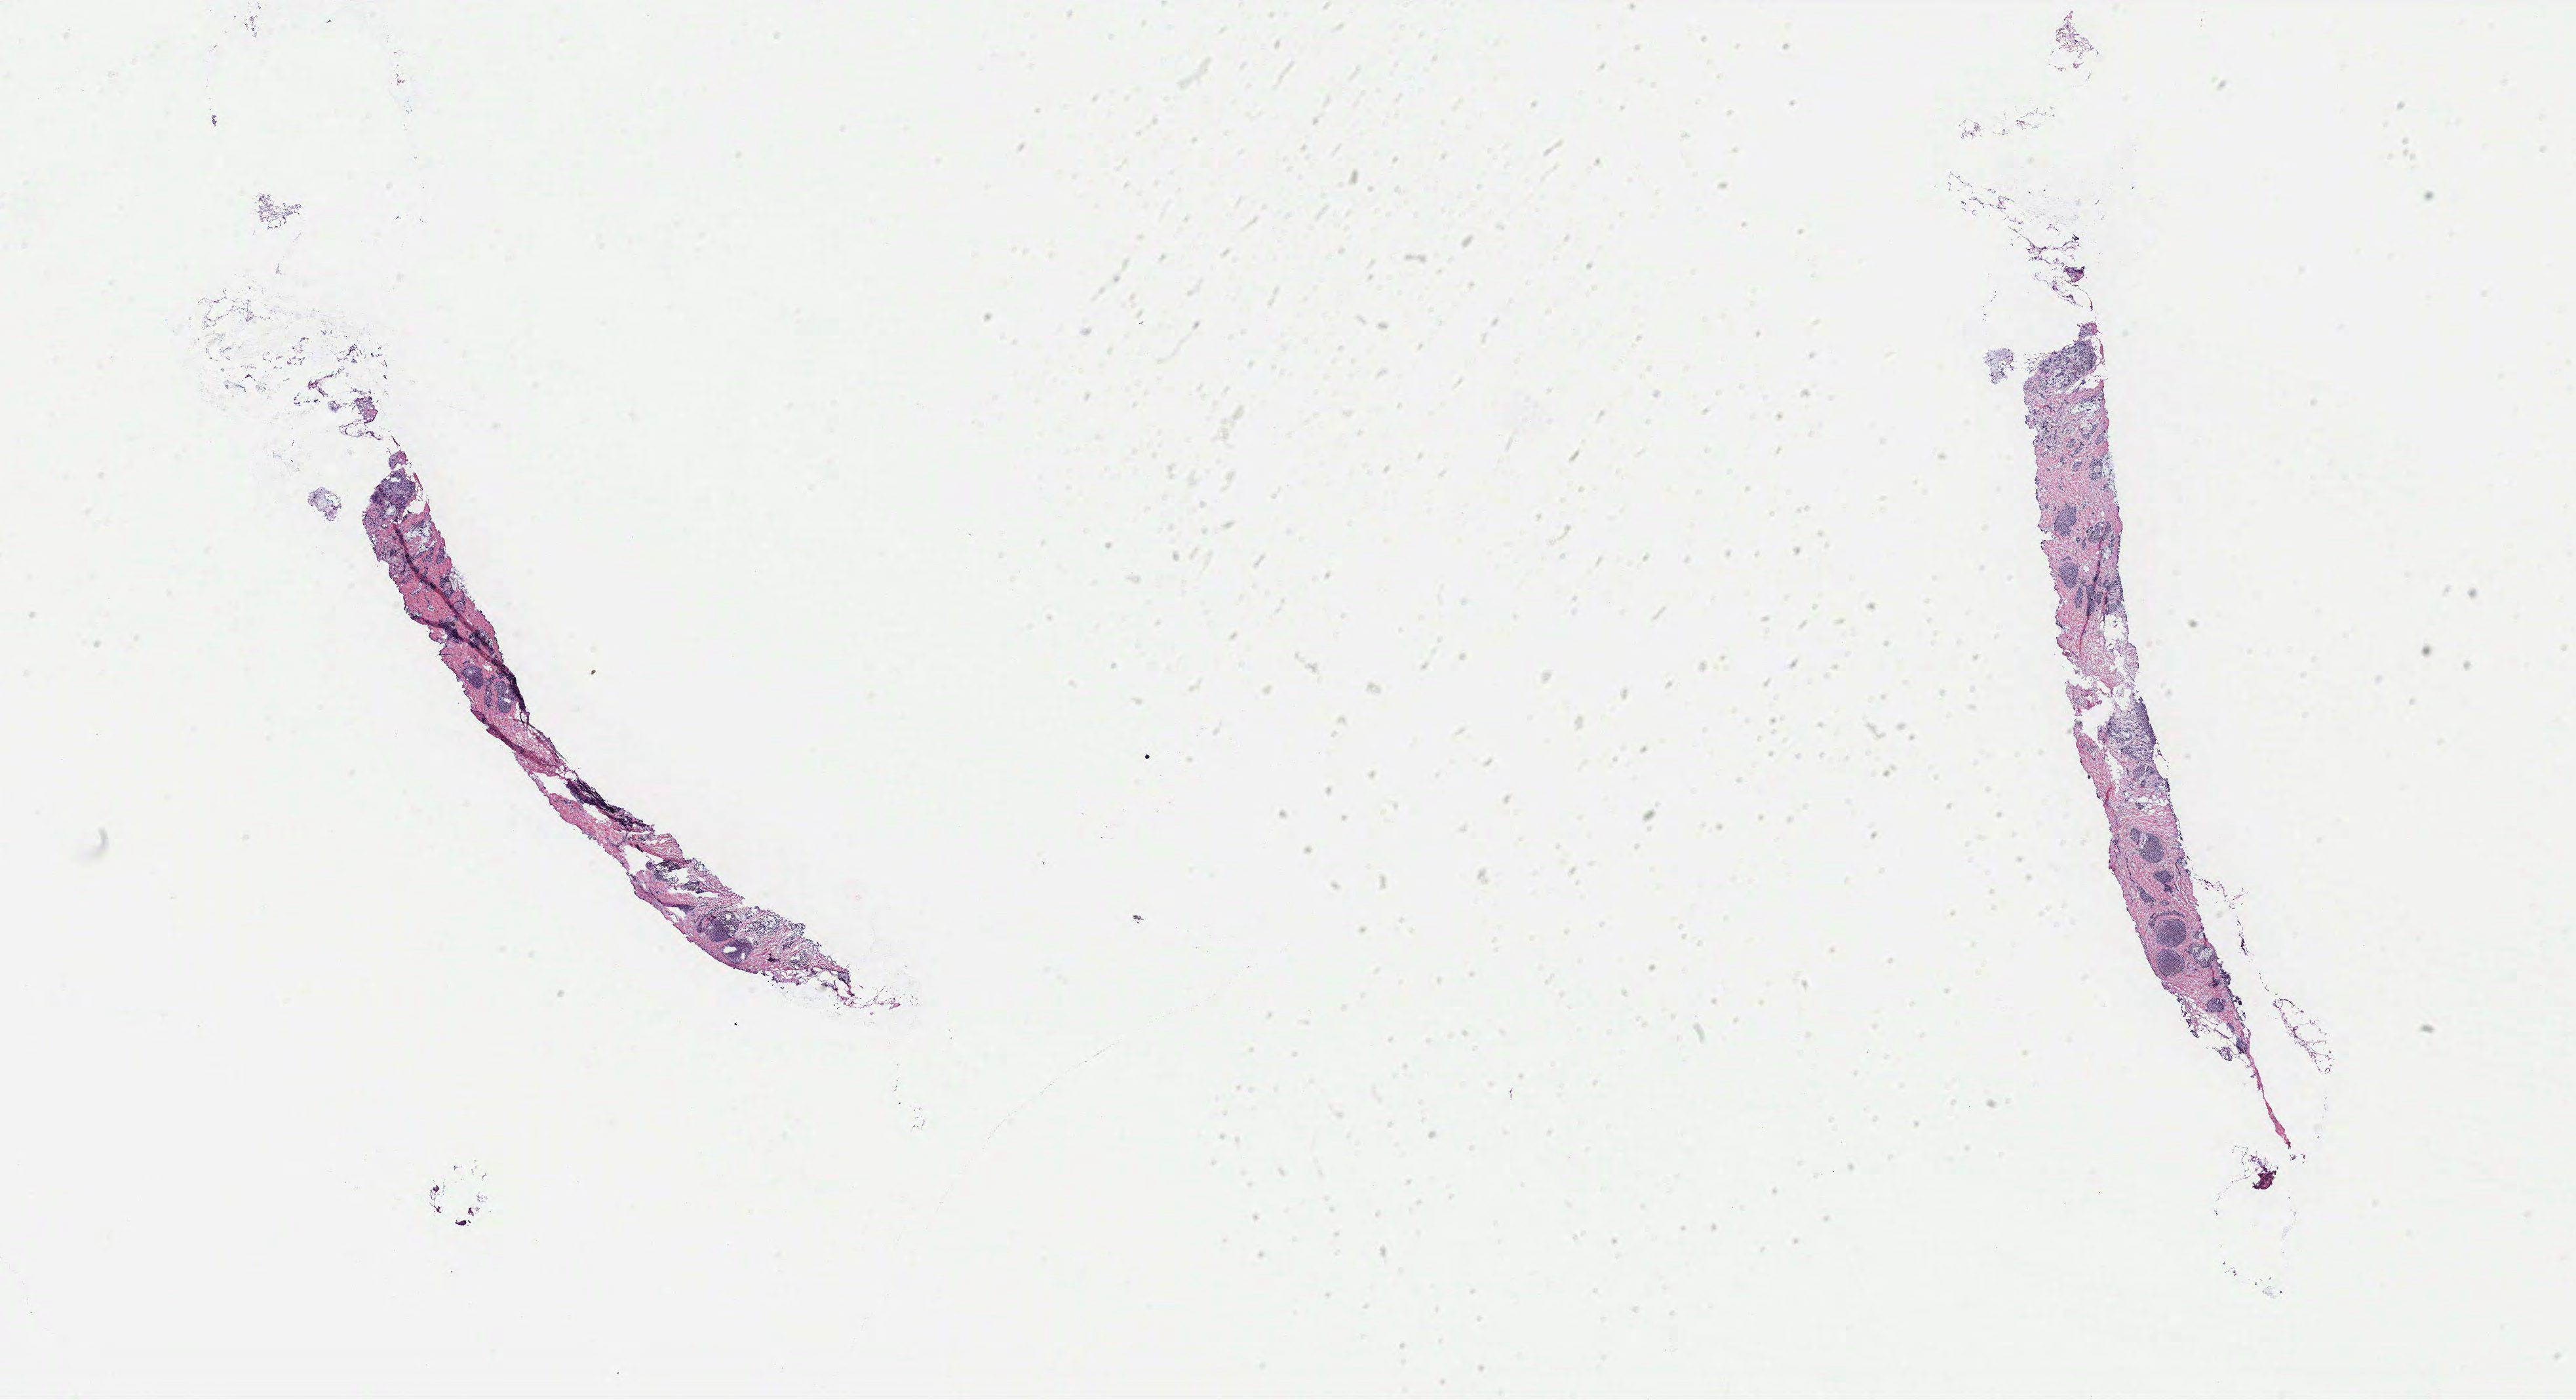
Hematoxylin and eosin (H&E) stained whole-slide image — low-resolution overview of the scanned area, about 31.5 x 17.1 mm, breast, tissue type not recorded.
Patient diagnosis (cohort enrolment): breast cancer (breast).